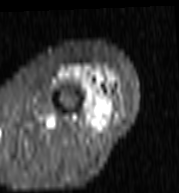
MRI of an extremity soft-tissue mass, one axial slice; slice 36 of 103 in the series (ordered by position); STIR; MR volume resampled by the dataset authors to the PET/CT grid (not the native acquisition matrix); 3.27 mm slice thickness; 179 × 193 image matrix, field of view 175 × 188 mm. Female patient. From the clinical record (not read from this slice): histological type: undifferentiated – high grade; grade: high; site of the primary tumour: left thigh.
Outlined on this slice (expert contour drawn on MRI and transferred to this co-registered scan by the dataset authors):
- gross tumour volume including surrounding oedema: bounding box (x1, y1, x2, y2) in pixels: (61, 66, 122, 127)